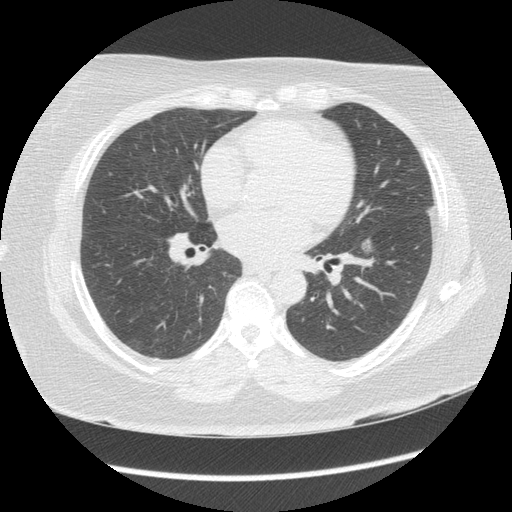
Low-dose screening chest CT, one axial slice; position 67 of 144 along the scan axis; 120 kVp; lung window (W 1500 / L -600 HU); 2.5 mm slice thickness; 512 × 512 image matrix.
Annotated regions visible in this slice (manually delineated by an expert):
- lesion 1 (tumor, lower lobe of left lung): box from (x=361, y=238) to (x=373, y=254) px